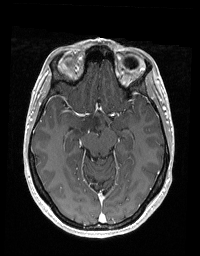
Brain MRI from a brain-tumour surgery series, one axial slice. Position 114 of 192 along the scan axis. T1-weighted post-contrast. 1 mm slice thickness. 200 × 256 image matrix, field of view 195 × 250 mm. Case-level facts recorded for this patient, not image findings: histopathology: Glioblastoma; WHO grade: 2; IDH mutation: no.
Structures marked on this image (manually delineated by an expert):
- tumour: bounding box <74,115,99,137> (left, top, right, bottom; pixels)